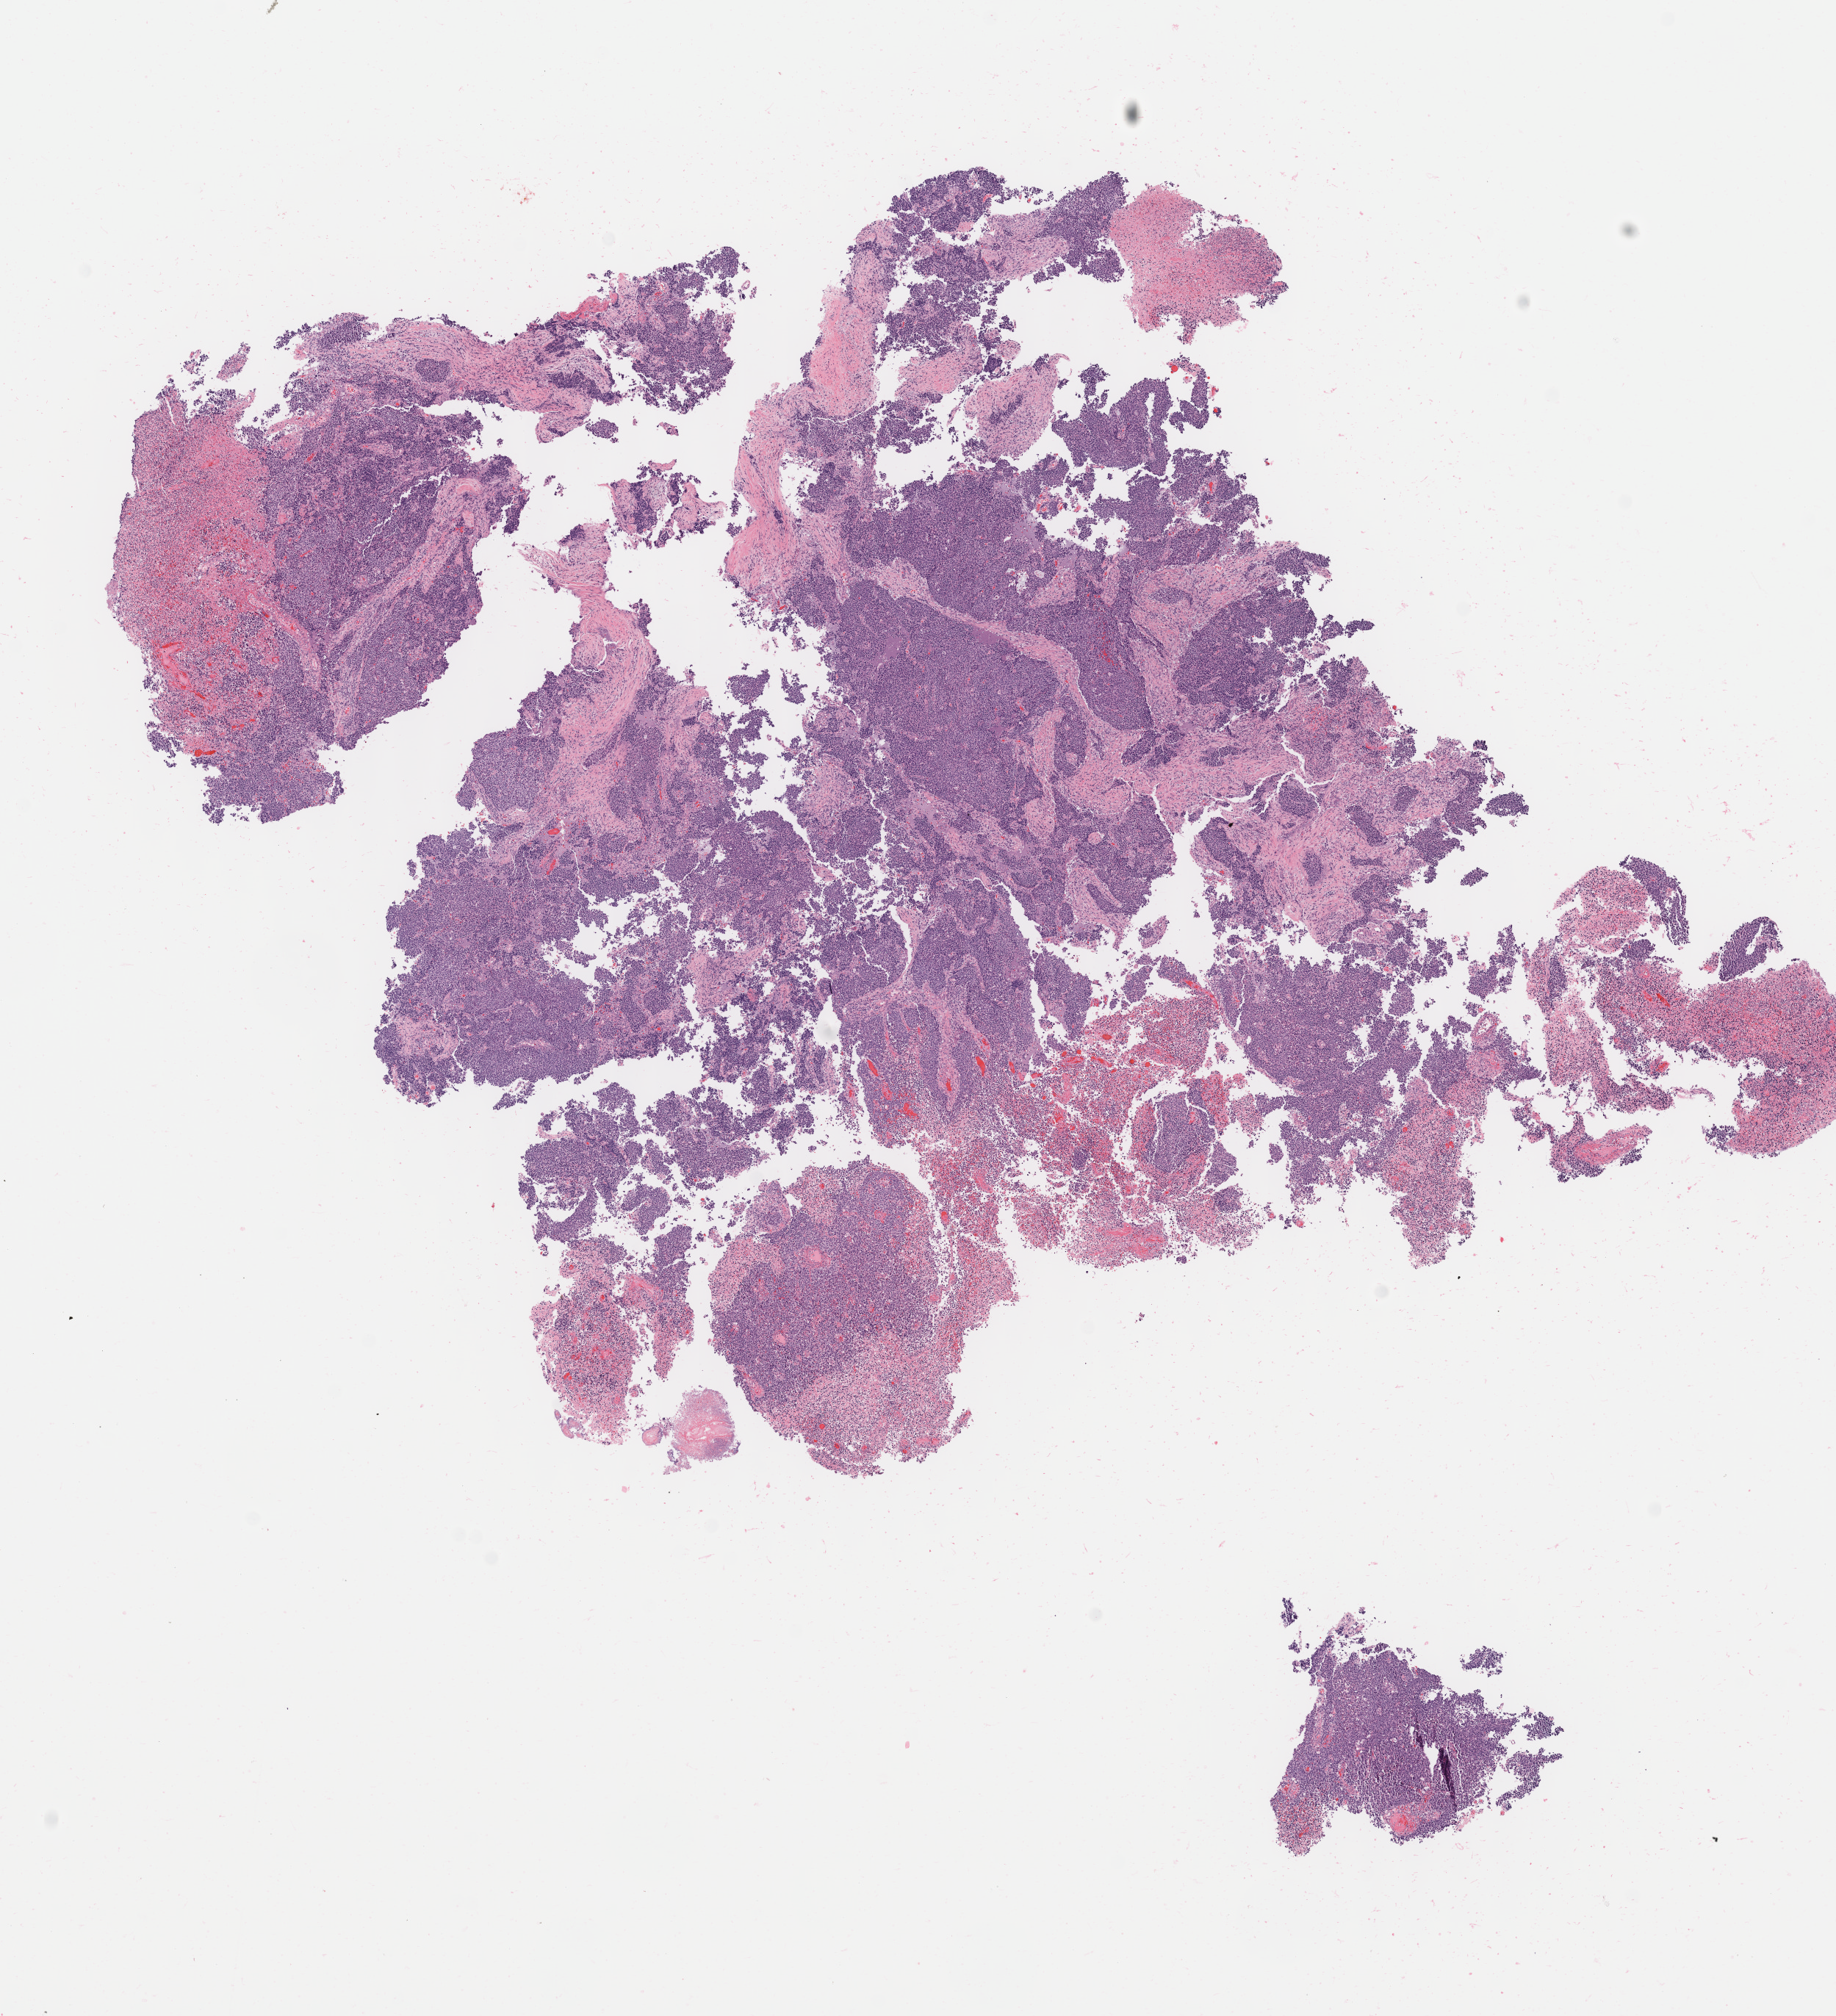
Digitized H&E-stained section — whole scanned area (about 9.9 x 10.9 mm) shown as a low-resolution overview, tumor tissue, anatomic site: cervix. Patient female; age 41 years.
Histologic diagnosis: Small cell carcinoma, NOS.